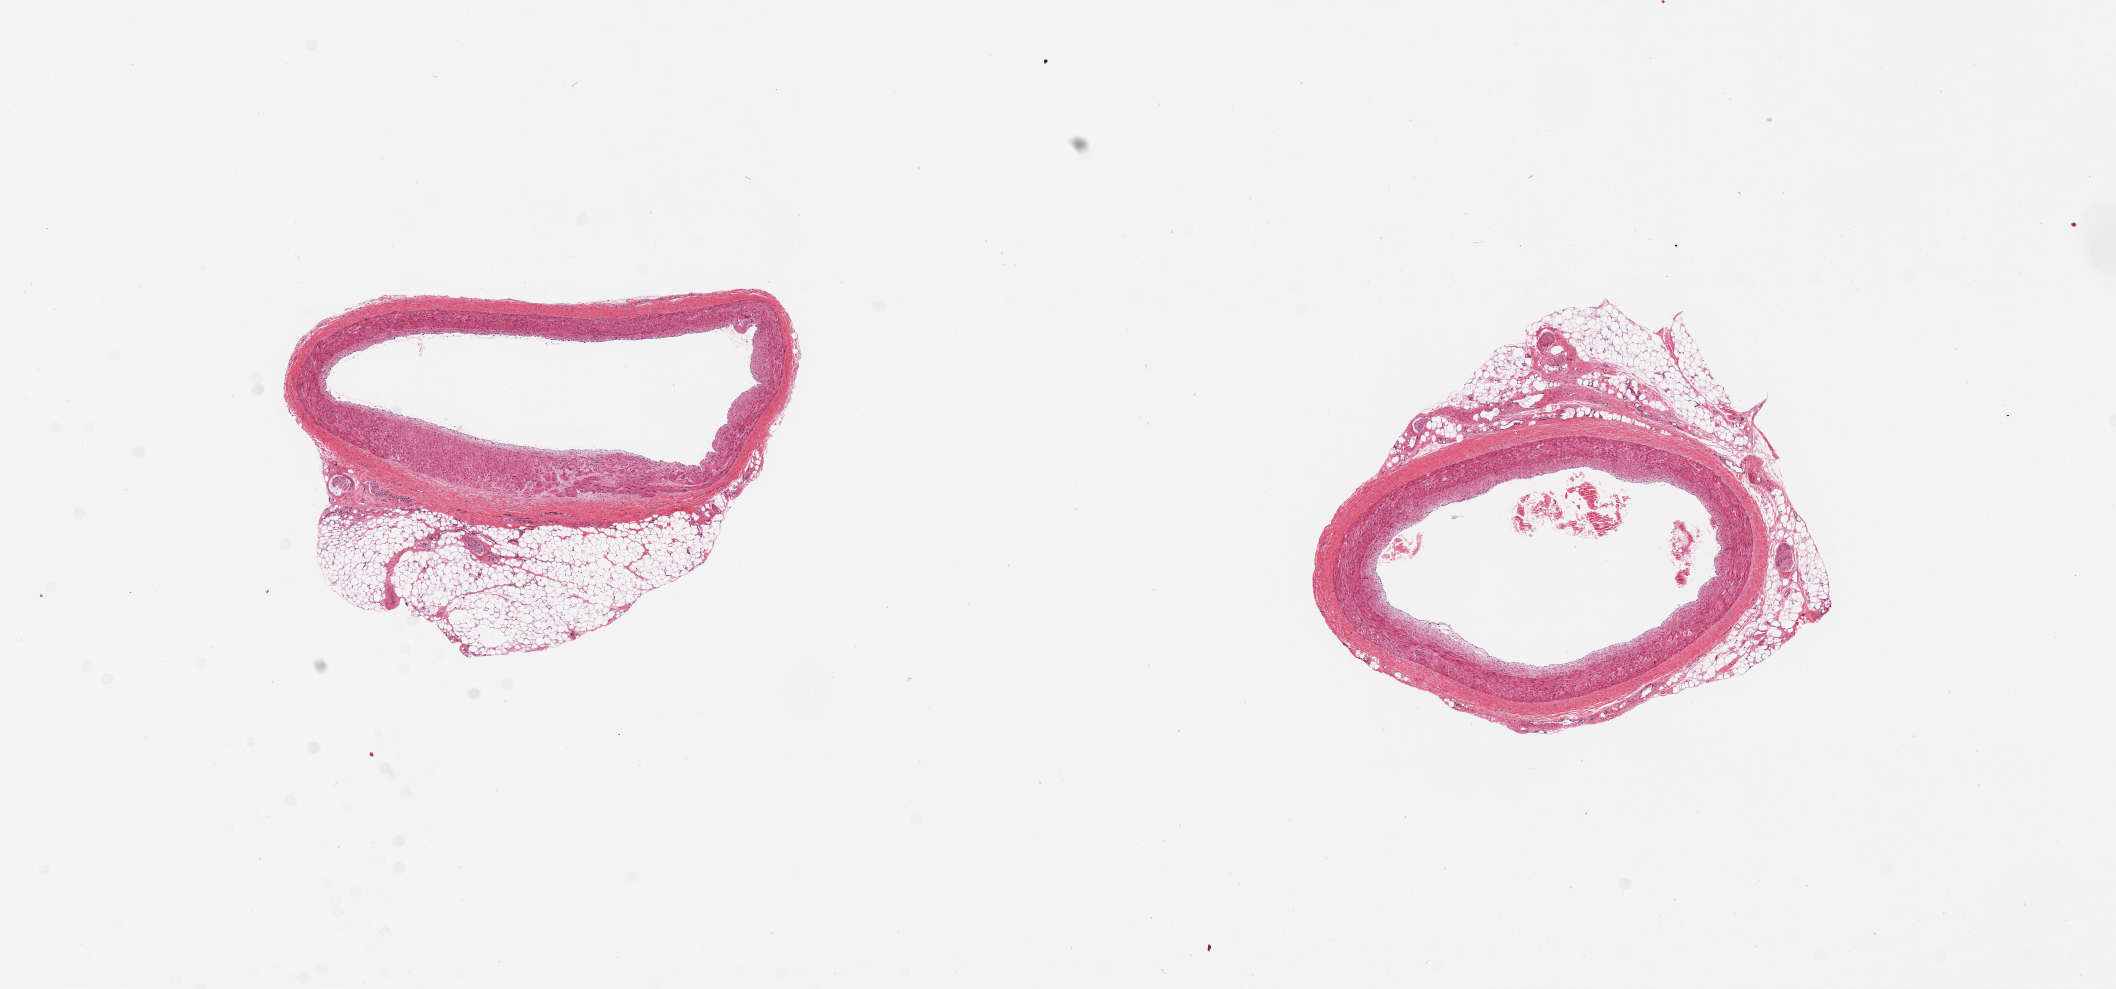
Digitized hematoxylin and eosin (H&E)-stained section — shown as a low-resolution overview of the whole scanned area (about 16.7 x 7.8 mm, slide scanned at 20x); PAXgene-fixed, paraffin-embedded tissue; section of coronary artery (target tissue); donor tissue sample. Donor: female.
Pathologist's review note for this sample: 2 pieces, 25% external fat.